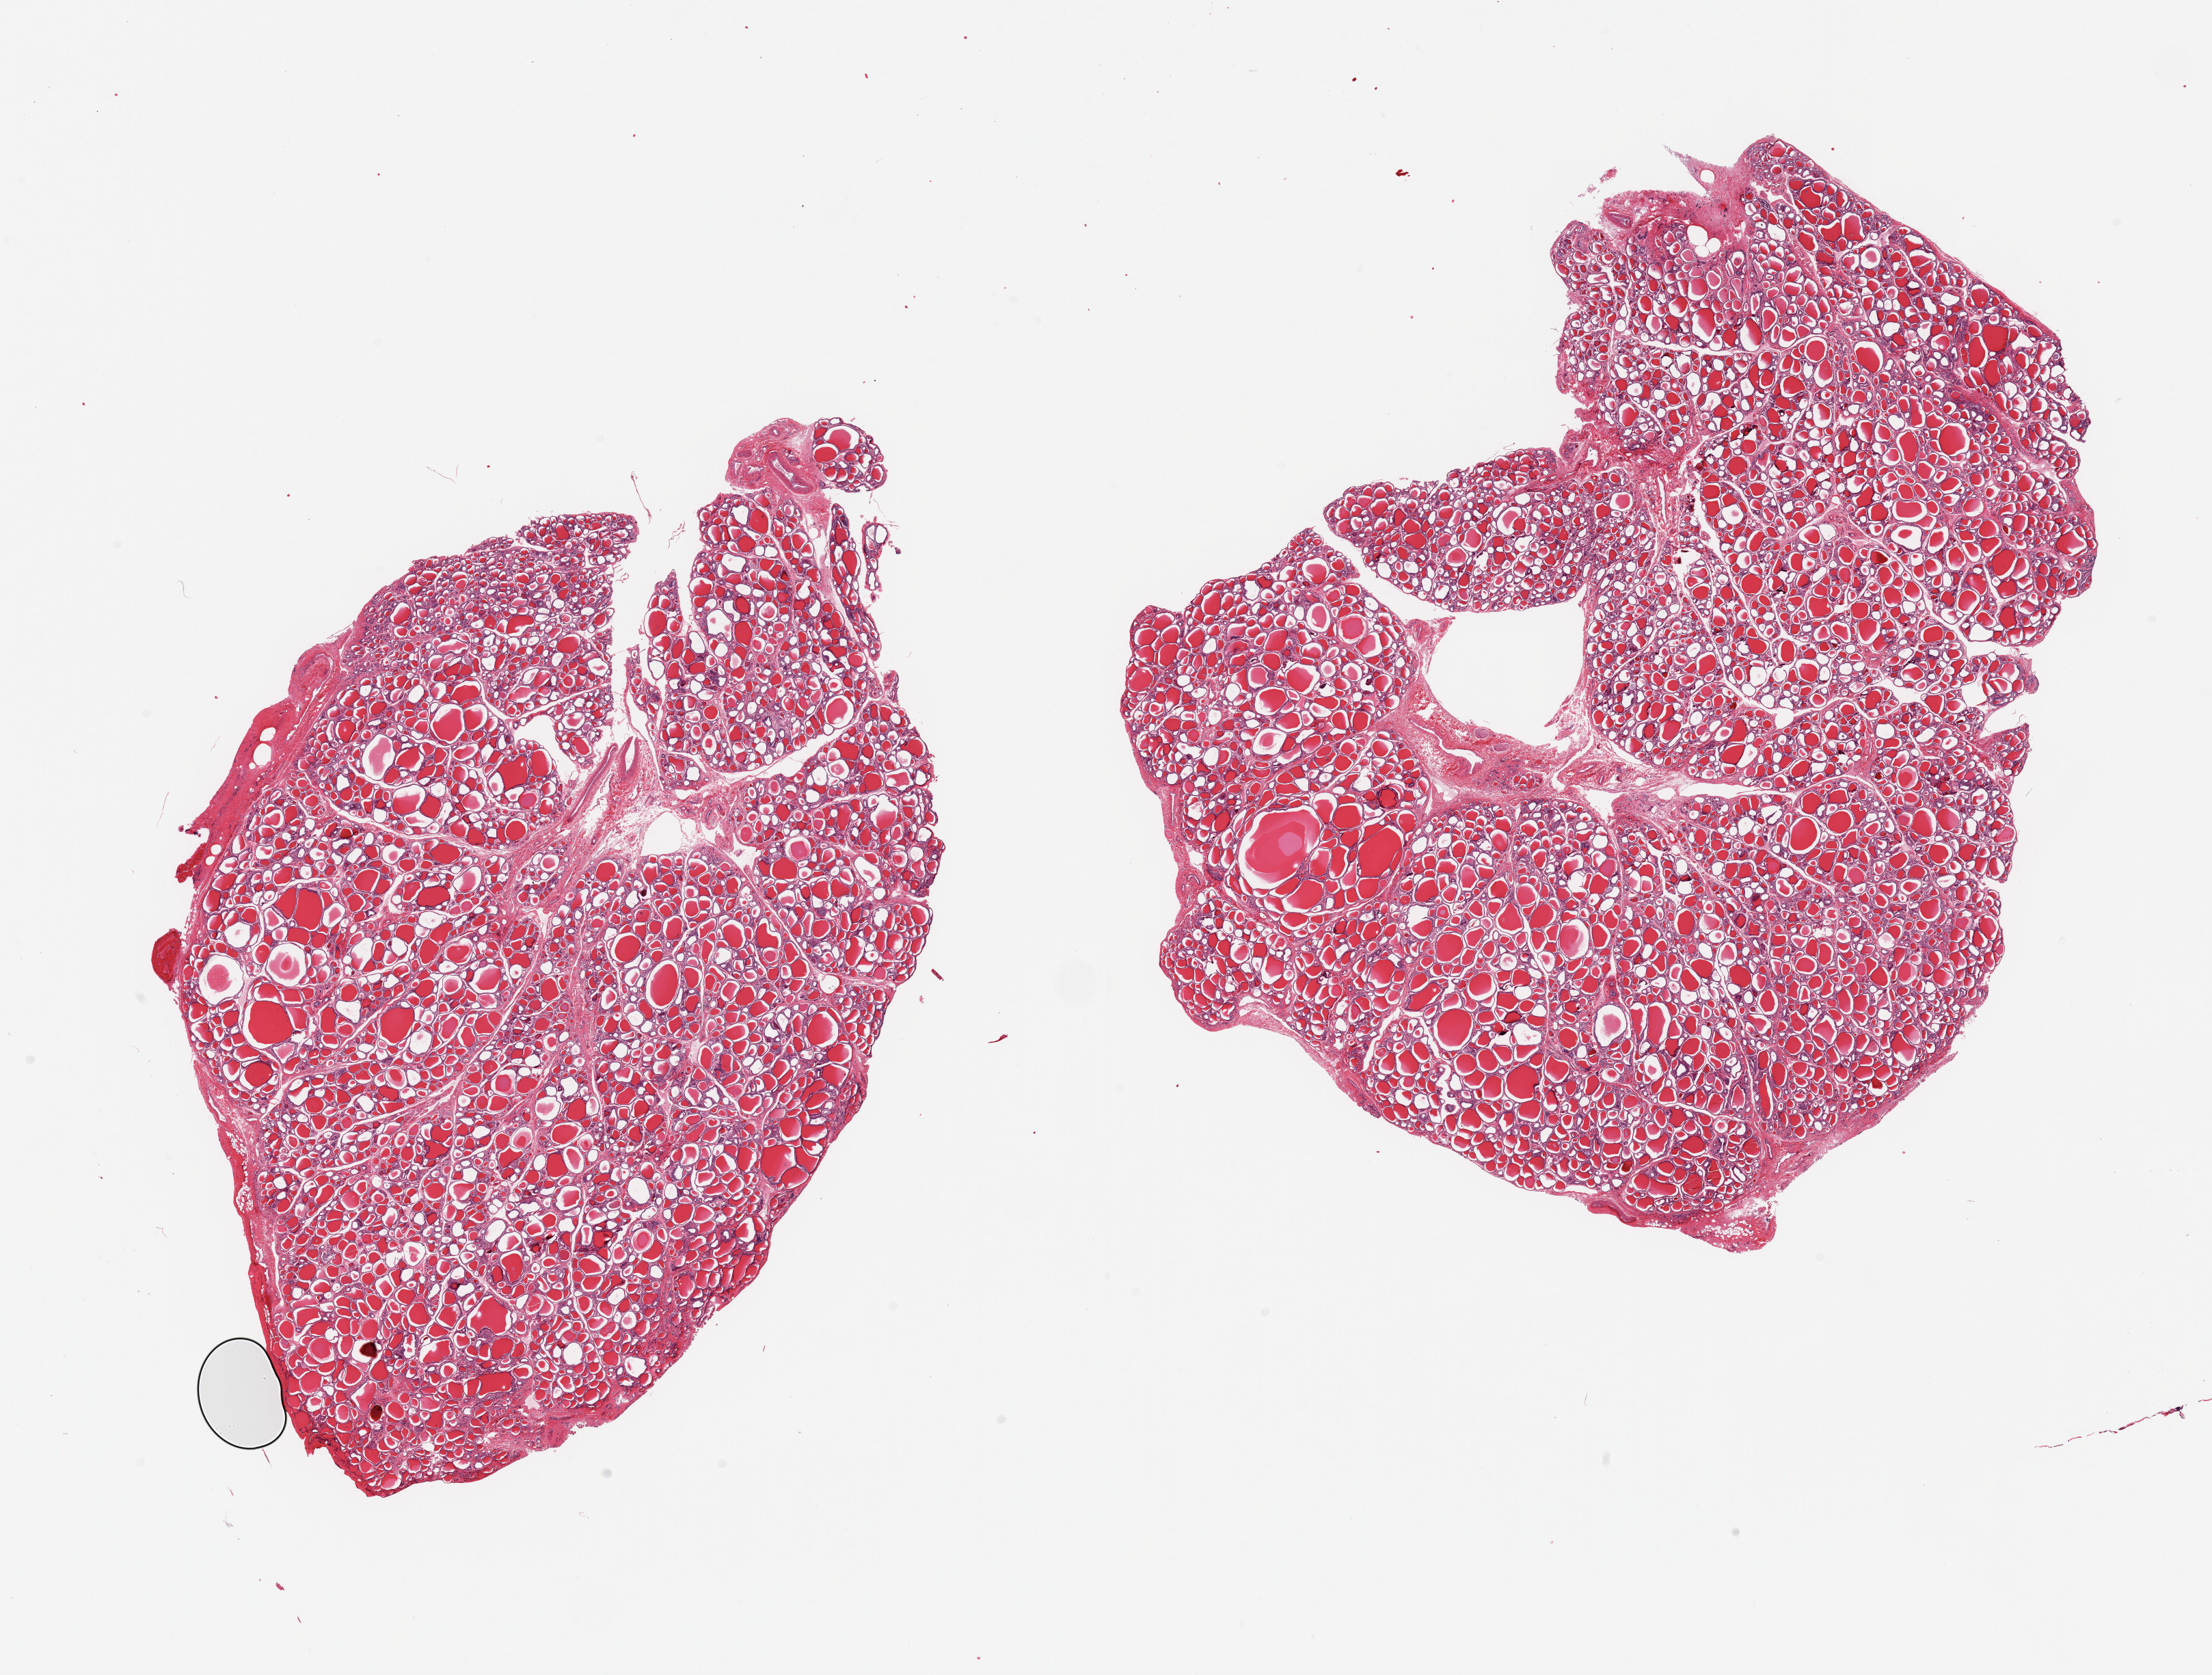
Digitized H&E-stained section, brightfield — whole scanned area (about 25.6 x 19.4 mm, from a 20x scan) shown as a low-resolution overview, PAXgene-fixed, paraffin-embedded tissue, target tissue: thyroid, tissue donor sample. Donor: male.
- pathologist's review note for this sample: 2 pieces; trivial attachment of fibrous tissue/skeletal muscle